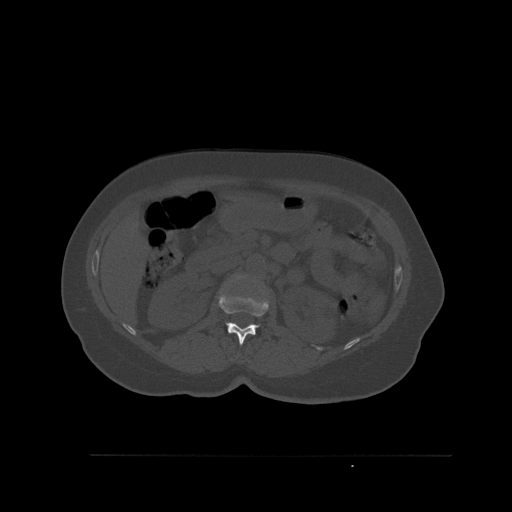
CT including the spine, one axial slice; slice 262 of 527 in the series (ordered by position); bone window (W 1800 / L 400 HU); 512 × 512 image matrix, field of view 470 × 470 mm. Patient: female, 73 years. Case-level facts recorded for this patient, not image findings: primary cancer: breast.
Structures marked on this image (semi-automatic segmentation, software-assisted and operator-edited):
- L1 vertebra: bounding box <218,294,277,345> (left, top, right, bottom; pixels)